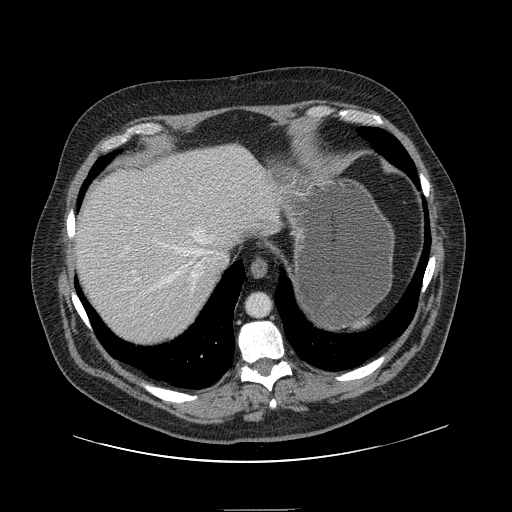
Contrast-enhanced abdominal CT, one axial slice; position 123 of 154 along the scan axis; 120 kVp; intravenous contrast given; soft-tissue window (W 400 / L 40 HU); 2.5 mm slice thickness; 512 × 512 image matrix, field of view 451 × 451 mm. Male patient, age 61 years. Case-level facts recorded for this patient, not image findings: diagnosis: colorectal cancer liver metastases, imaged before liver resection; multiple liver metastases: yes; largest metastasis: 2.6 cm; disease in both lobes: yes.
Outlined on this slice (outlined manually by an expert reader):
- hepatic veins: box from (x=120, y=229) to (x=211, y=292) px
- liver: (x=75, y=146)–(x=278, y=347)
- planned liver remnant (the part of the liver to remain after resection): (x=75, y=146)–(x=277, y=346)
- portal vein (with intrahepatic branches): (x=128, y=215)–(x=138, y=282)